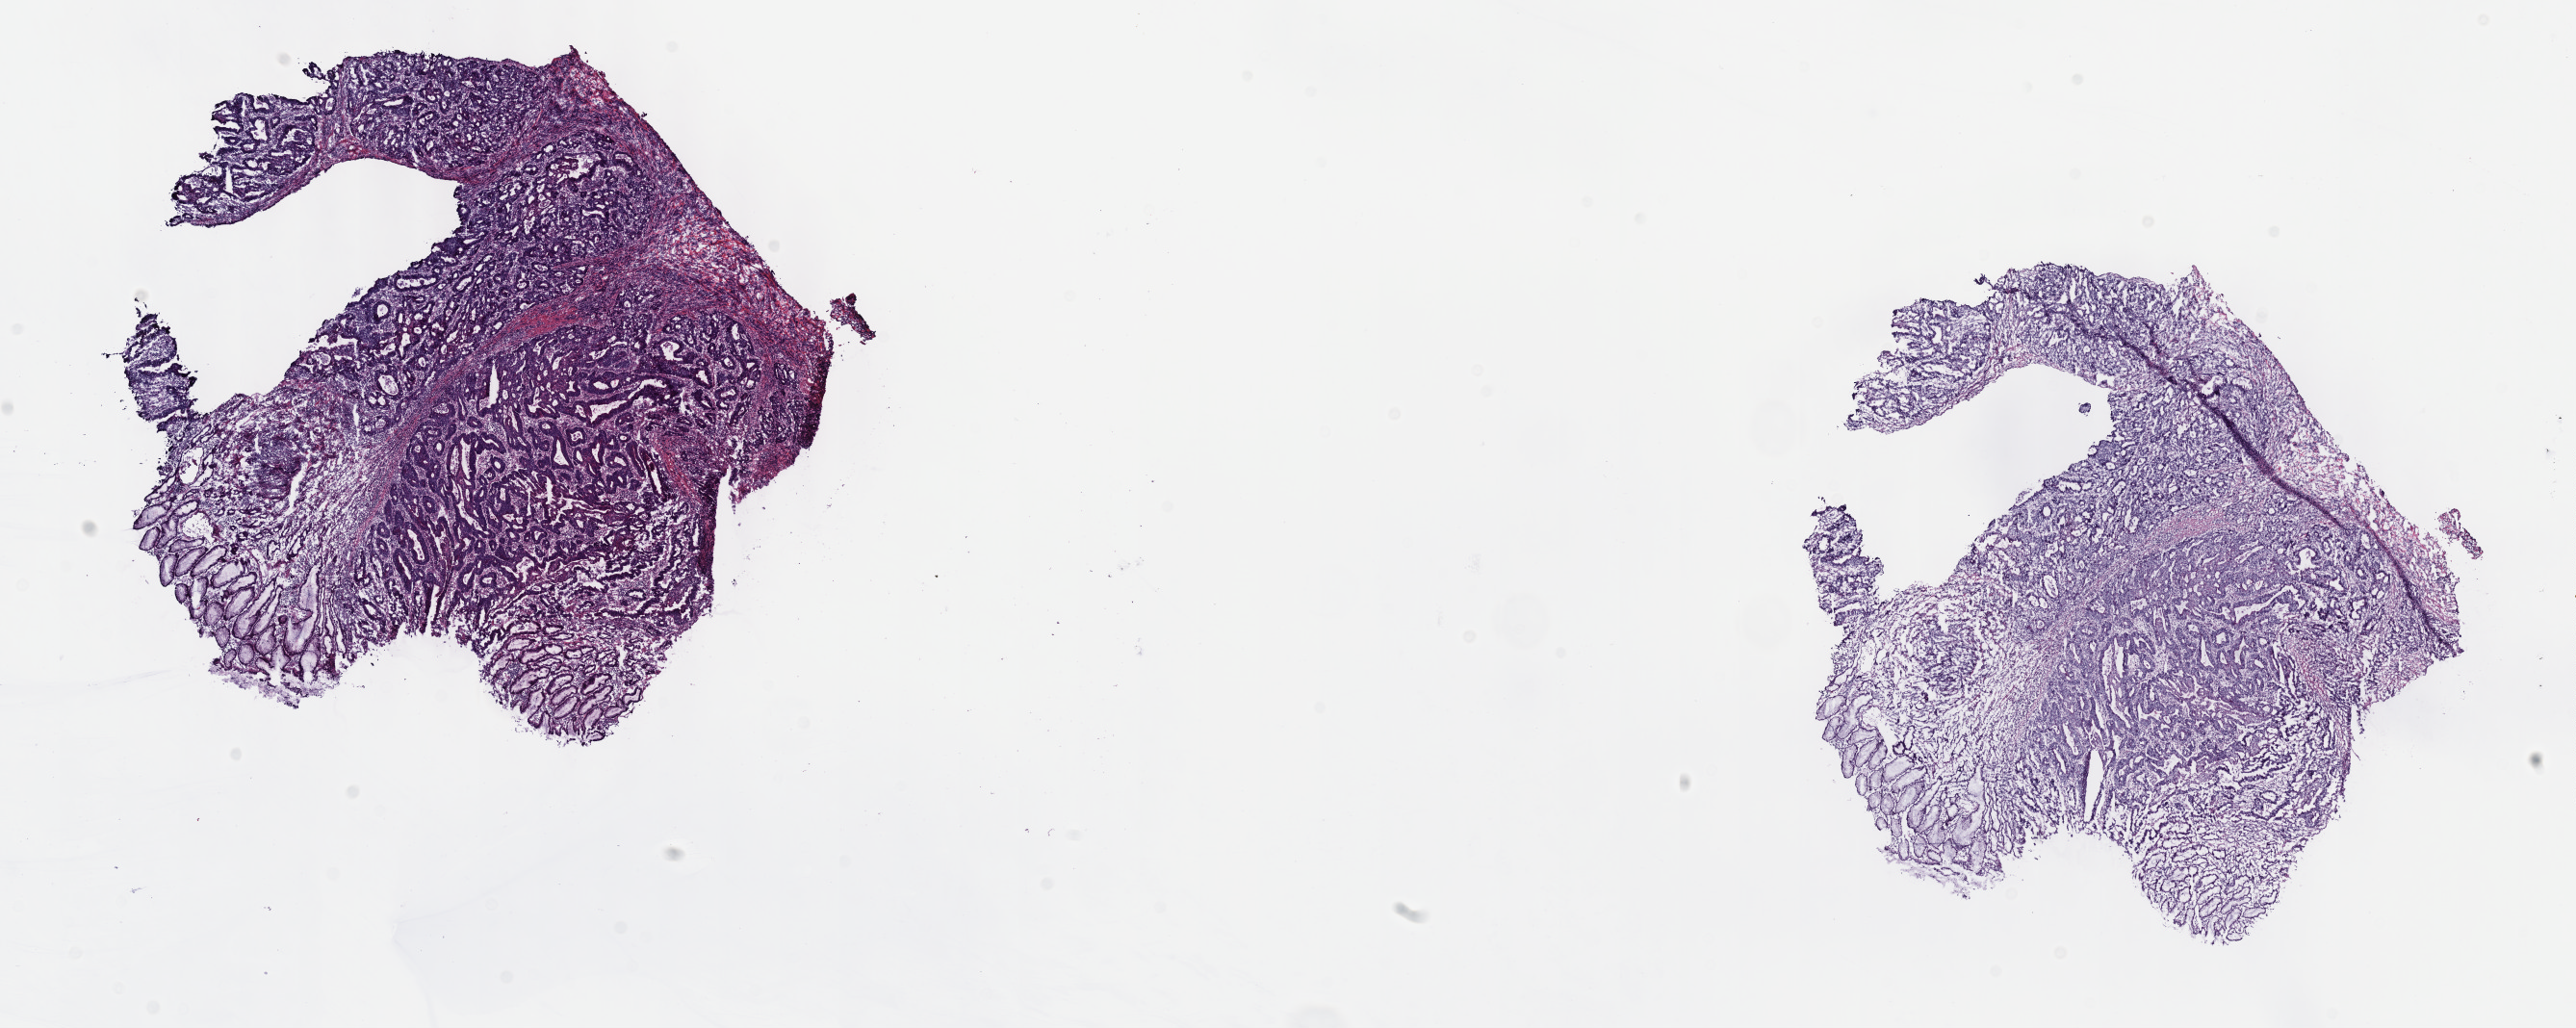
Digitized Hematoxylin and eosin (H&E) stained tissue section (whole slide), a low-resolution overview of the entire scanned area, about 21.6 x 8.6 mm. Frozen section. Sample: primary tumour, stomach. Patient: male, age at initial diagnosis 78 years. Histologic grade: G2 (moderately differentiated). Pathologist review of this section (percent, as recorded): tumour cells 90%, tumour nuclei 65%, normal cells 10%, stromal cells 0%, necrosis 0%. Inflammatory infiltration, as recorded: lymphocyte infiltration 5%, monocyte infiltration 0%, neutrophil infiltration 0%.
* lymph nodes positive (case pathology): 2 of 24 examined
* AJCC pathologic stage: IIIA
* diagnosis: Adenocarcinoma, intestinal type (cardia, NOS)